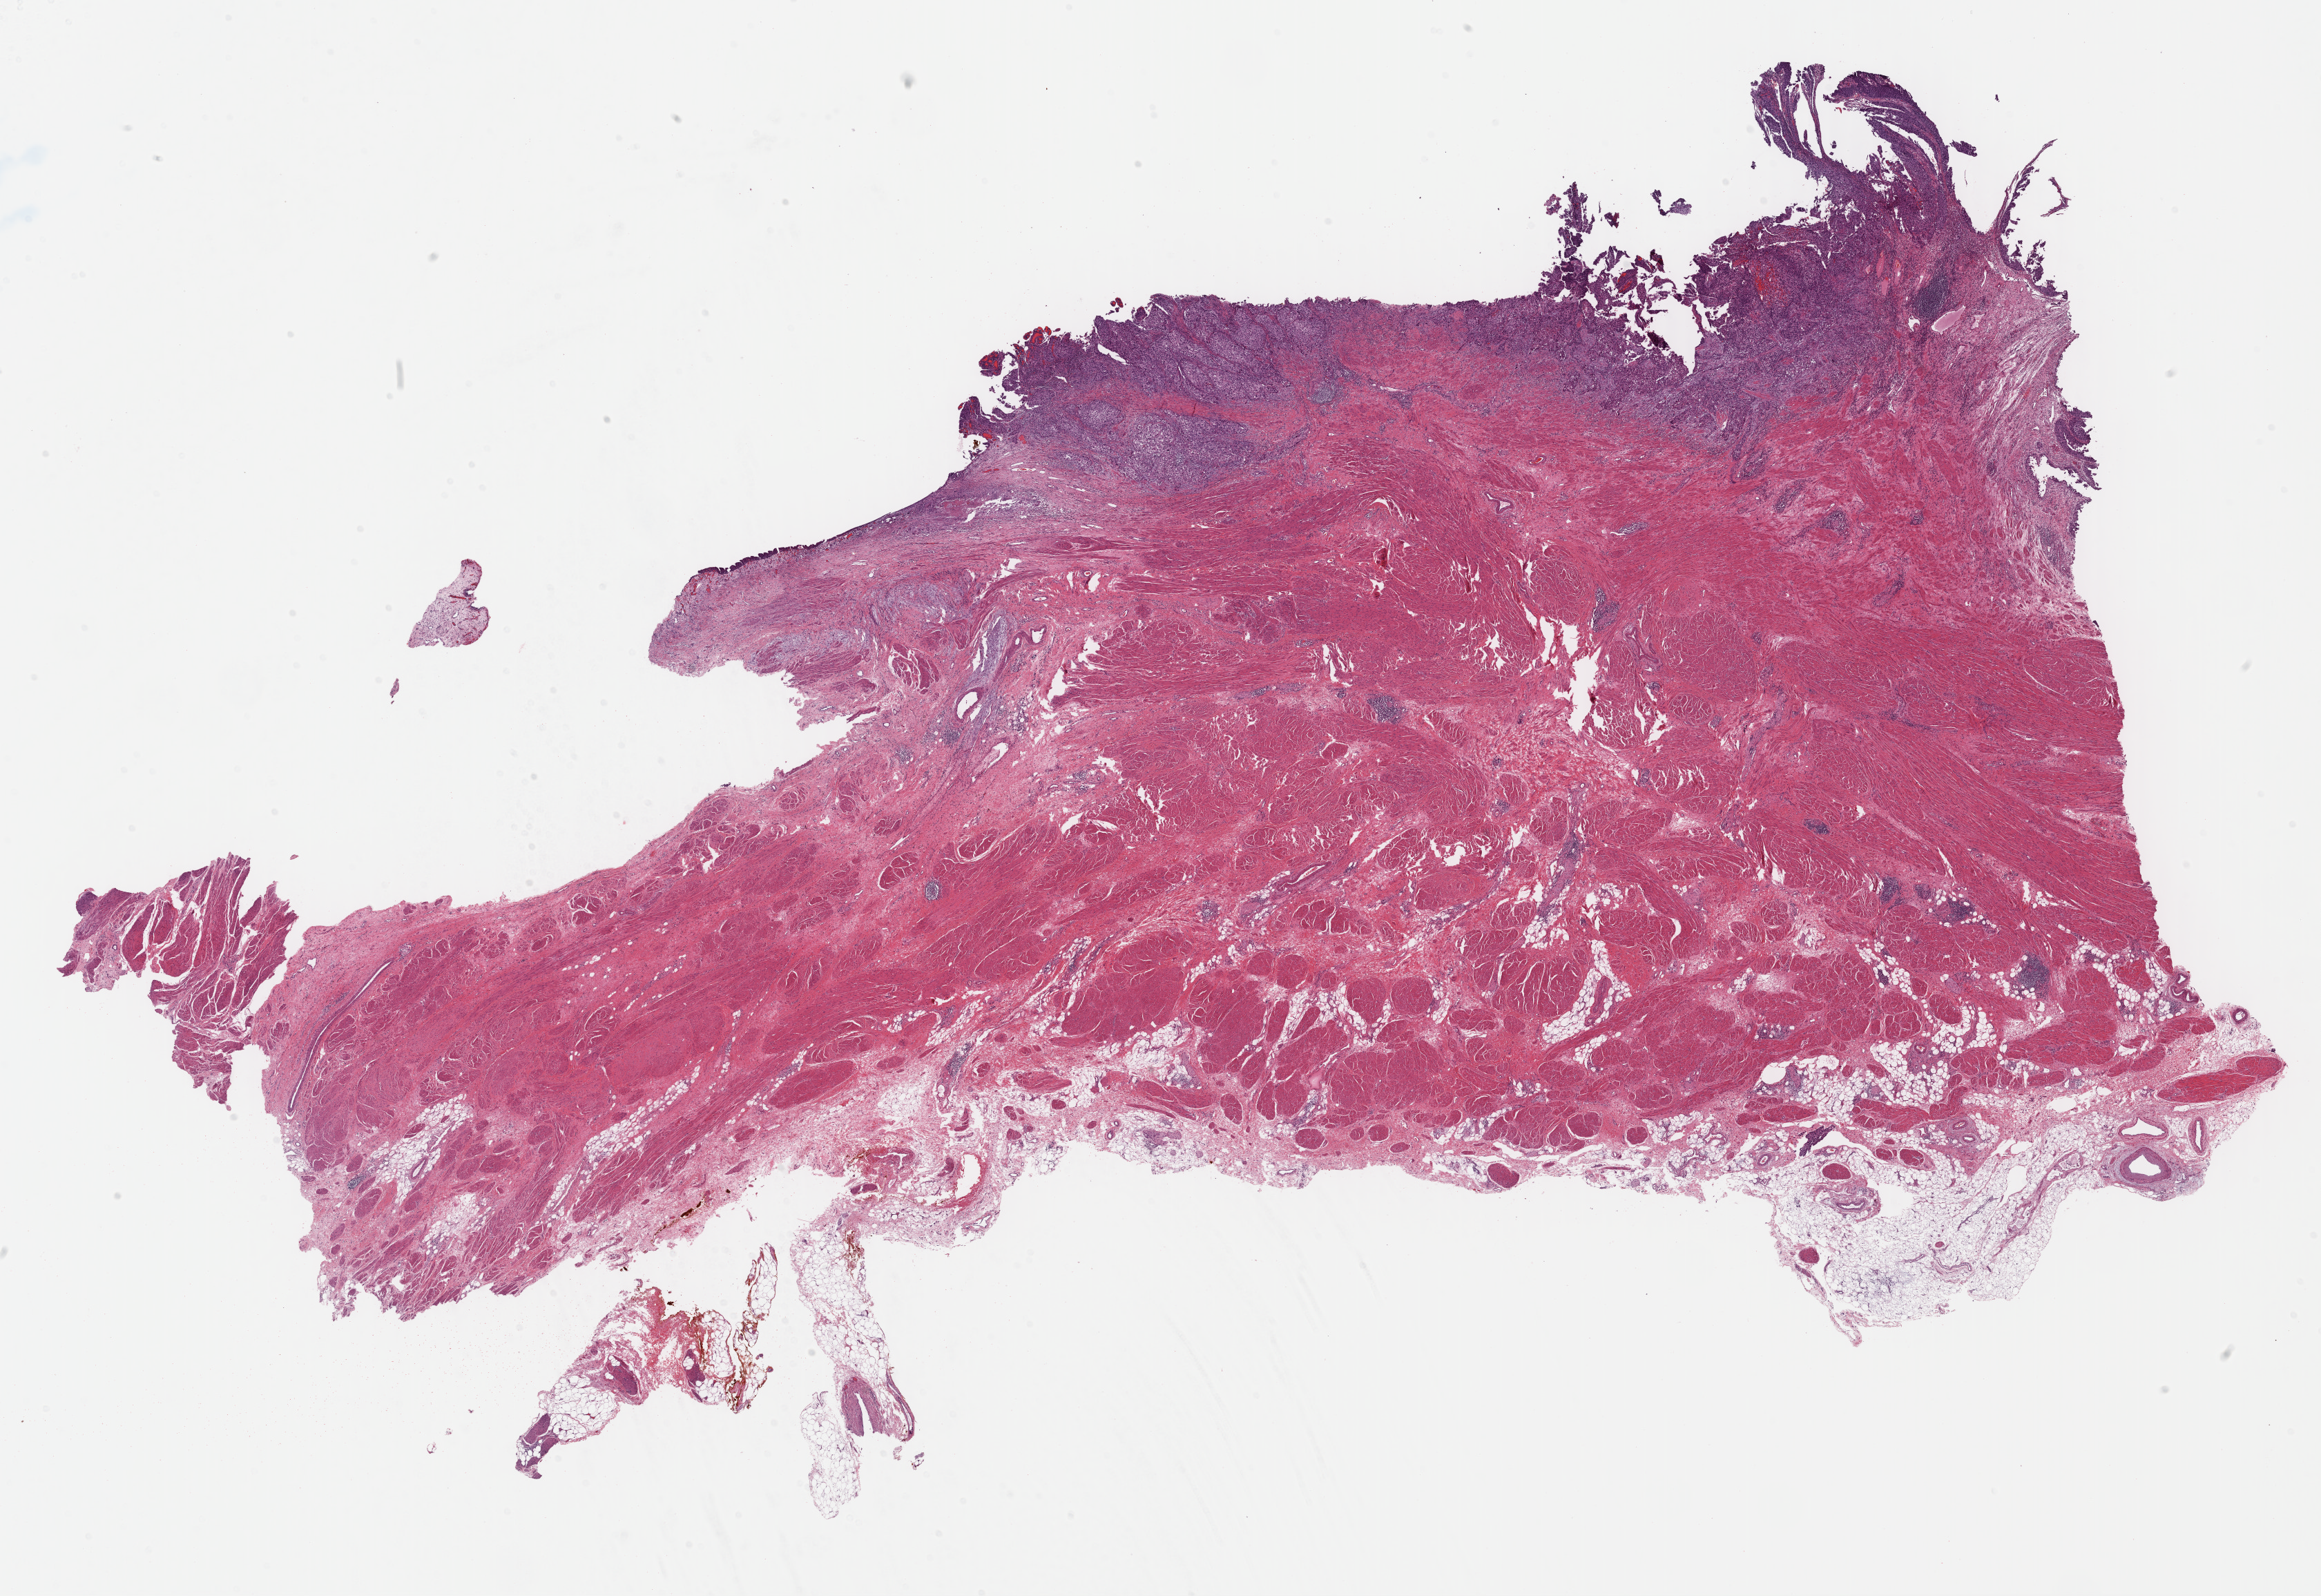
Whole-slide histology image, H&E-stained — a low-resolution overview of the entire scanned area, about 26.4 x 18.2 mm (acquisition: 40x scan), formalin-fixed paraffin-embedded (FFPE) diagnostic section, bladder, primary tumour sample. Male patient; age at initial diagnosis 64 years. Histologic grade: high grade.
AJCC pathologic stage: II (7th edition). Histologic diagnosis: Papillary transitional cell carcinoma (lateral wall of bladder).